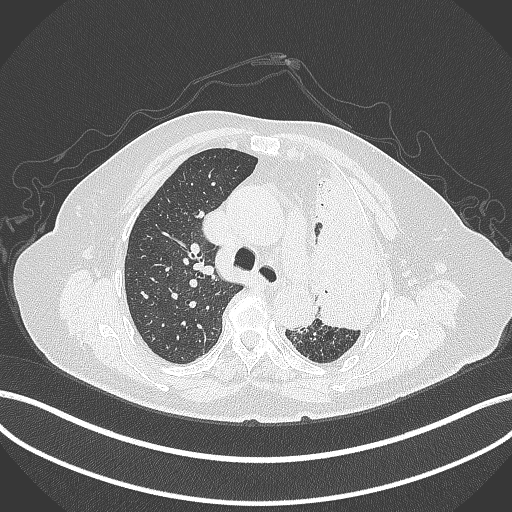
Chest CT, one axial slice; position 273 of 399 along the scan axis; reconstruction kernel B70f; 120 kVp; lung window (W 1500 / L -600 HU); 1 mm slice thickness; 512 × 512 image matrix, field of view 400 × 400 mm. Patient: female, 75 years. From the clinical record (not read from this slice): clinical TNM (as recorded): T3 N3 M1.
Annotated regions visible in this slice (bounding box drawn by a radiologist):
- lung tumour (recorded histology: adenocarcinoma): bounding box (x1, y1, x2, y2) in pixels: (301, 149, 394, 335)